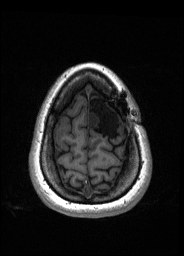
Pre-operative brain MRI before brain-tumour surgery, one axial slice. Slice 37 of 176 in the series (ordered by position). T1-weighted post-contrast. 184 × 256 image matrix, field of view 180 × 250 mm. From the clinical record (not read from this slice): histopathology: Oligodendroglioma; WHO grade: 2; IDH mutation: yes; tumour location: Left Frontal.
Annotated regions visible in this slice (expert manual segmentation):
- tumour: bounding box [x1, y1, x2, y2] px = [88, 112, 99, 128]